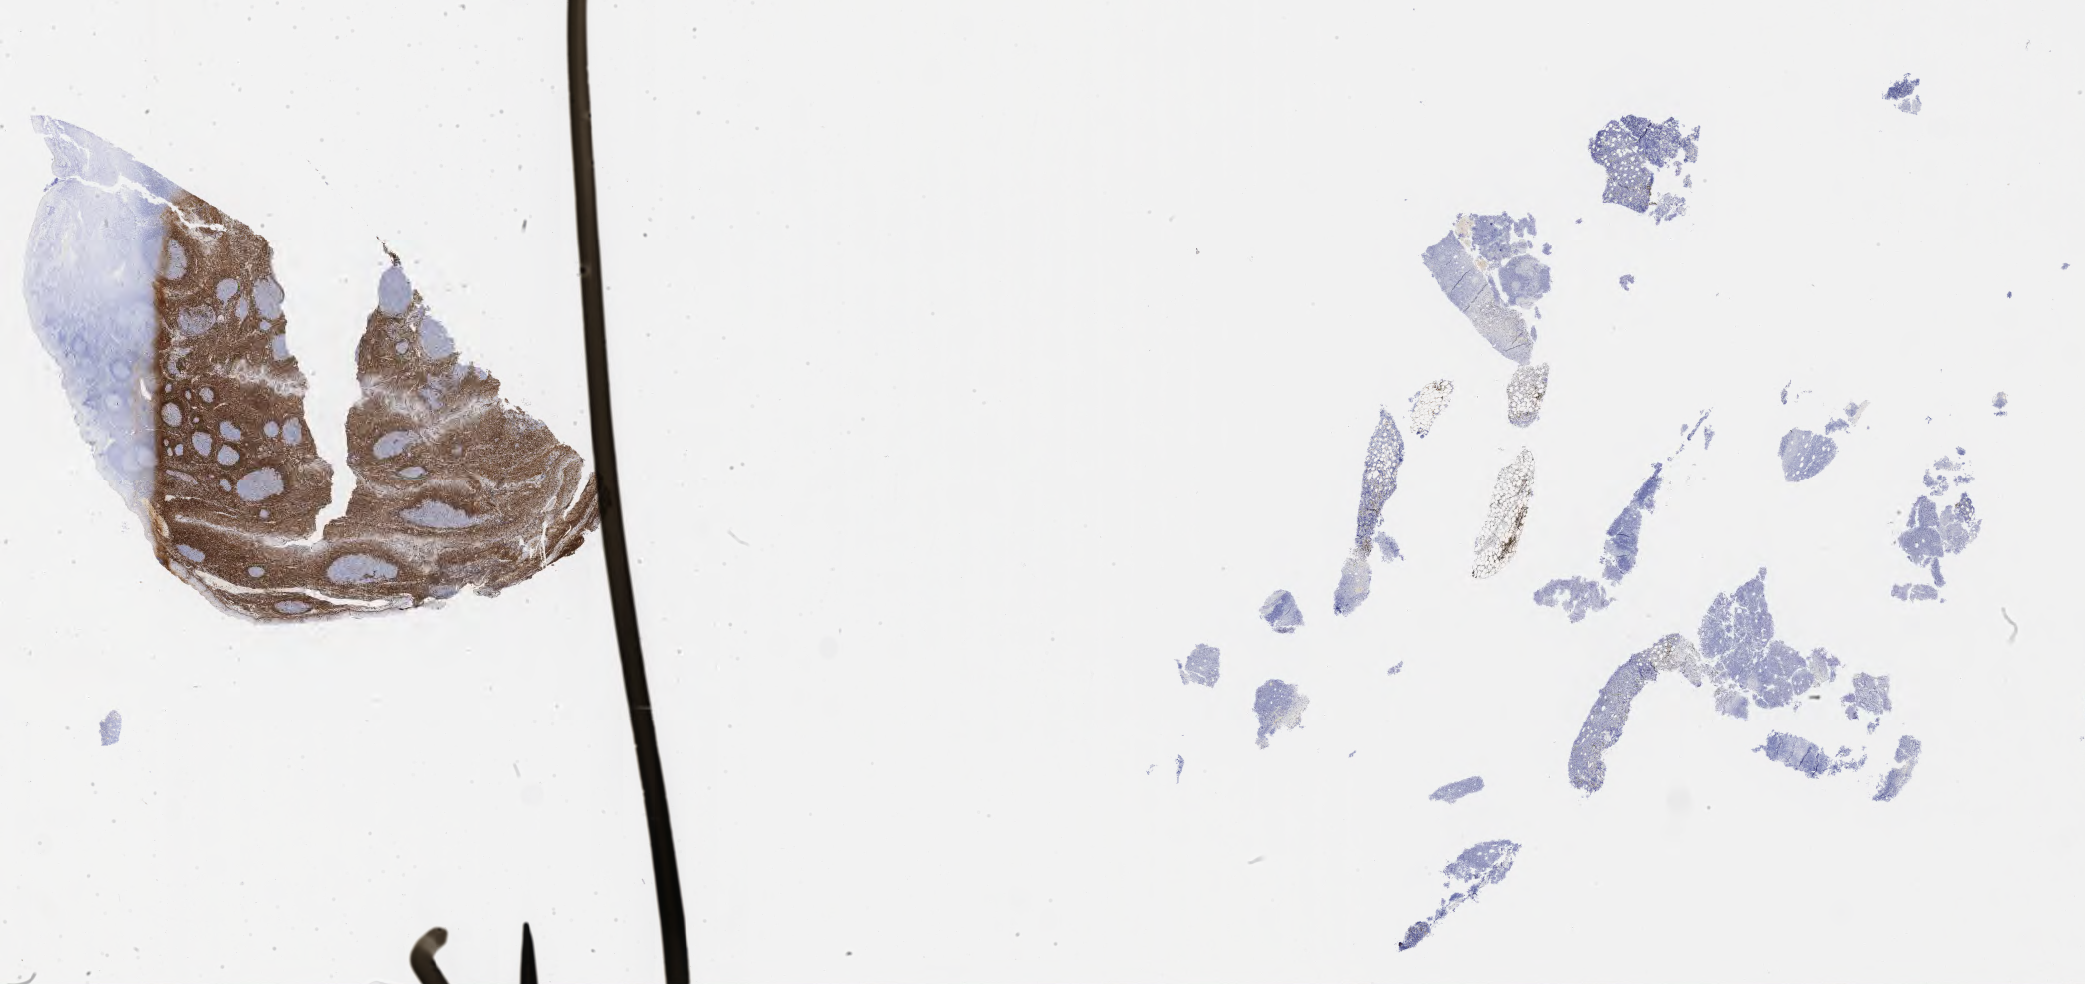
IHC for BCL2, whole-slide image, whole scanned area (about 33.7 x 15.9 mm) shown as a low-resolution overview; tumor tissue; anatomic site: pelvis. Patient female; 64 years old.
Diagnosis: Burkitt lymphoma, NOS.